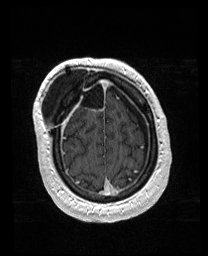
Brain MRI from a brain-tumour surgery series, one axial slice; slice 39 of 176 in the series (ordered by position); T1-weighted post-contrast; 1 mm slice thickness; 208 × 256 image matrix, field of view 208 × 256 mm. Case-level facts recorded for this patient, not image findings: histopathology: Astrocytoma; WHO grade: 4; IDH mutation: yes; tumour location: Right Orbitofrontal Anterior Temporal Insular.
Outlined on this slice (expert manual segmentation):
- previous resection cavity: box from (x=64, y=81) to (x=87, y=108) px